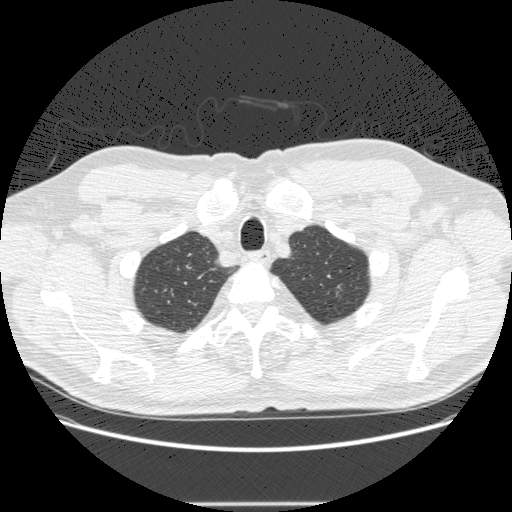
Chest CT (low-dose screening protocol), one axial image, baseline annual screen, lung window (W 1500 / L -600 HU), 1.25 mm slice thickness, 120 kVp, 512 × 512 image matrix, field of view 389 × 389 mm. Male, age 69 years at enrolment. Former smoker at enrolment.
- Expert reader's lesion annotation, bounding box <319,279,352,306> (left, top, right, bottom; pixels).
- Screening reader's record for this exam: no non-calcified nodule ≥4 mm recorded.
- Official screen result: negative screen, significant abnormalities not suspicious for lung cancer.
- Lung cancer was diagnosed 828 days after this screen: adenocarcinoma, NOS, left upper lobe, moderately differentiated (G2), stage IA (AJCC 6th edition), 10 mm at pathology.